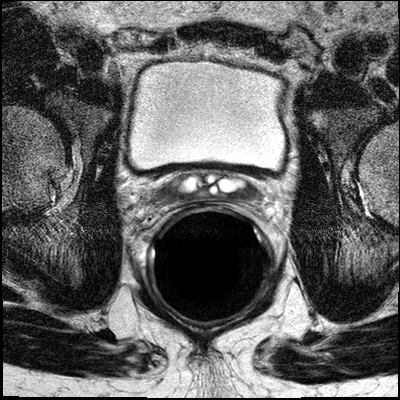
Prostate MRI examination; 3 images, each a single mid-volume slice chosen by position (not for content). Treatment context recorded for this patient: Surgery.
Image 1: axial T2-weighted image, slice 17 of 32.
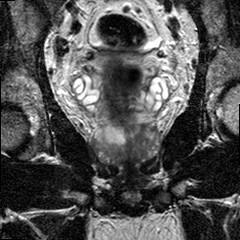
Image 2: coronal T2-weighted image, series "T2W_TSE_COR", slice 13 of 24.
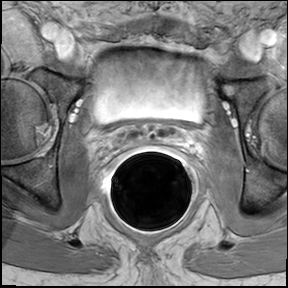
Image 3: DCE (dynamic gadolinium-enhanced) axial slice, series "AX BLISS_GAD_8", slice 17 of 32, dynamic phase 5 of 8, 6 mm slice thickness.
Report of this MRI examination:
FINDINGS: The prostate gland measures 4.8 (TV) x 3.1 (AP) x 3.3 (CC) cm and the prostate volume measures 25.5 cc.The zonal anatomy of the prostate gland is preserved. In the base and mid-third of the left posterolateral peripheral zone, geographic areas of low T2 hypointensity are visualized from the 4-6 o'clock positions with associated suspicious wash-in and washout genetics on dynamic postgadolinium images. The dominant nodule measures 1.8 (TV) x 0.8 (AP) cm in maximal dimension. The left posterolateral mass closely approximates the left neurovascular bundle with no definite involvement. No definite extracapsular involvement is seen. Rectum wall and Bladder neck are unremarkable. Mild benign prostatic hypertrophy and chronic prostatitis are visualized. The seminal vesicles are unremarkable. A small 4 mm round left perirectal lymph node is visualized to adjacent to the left obturator internus (slice location 48, series 601). No obturator or iliac lymphadenopathy. No suspicious bone marrow signal abnormalities are seen. Multiplanar reconstructions, subtraction images, and CAD analysis of the dynamic series for assessment of the kinetic information facilitated the interpretation of the exam. IMPRESSION:
1. Left posterolateral prostate cancer involving the base and middle third of the gland without evidence of extraglandular disease. No MRI evidence of neurovascular bundle involvement or seminal vesicle involvement. No pelvic lymphadenopathy. 2. Mild benign prostatic hypertrophy and moderate chronic prostatitis.

Prostate biopsy pathology (as recorded):
The specimen consists of multiple core fragments of brown/tan tissue measuring 0.2cm to 1.5cm in length and 0.1cm in diameter. The specimen is submitted entirely in seven cassettes.1-right pz, 2-right pz/tz, 3-right apex, 4-left pz, 5-left pz/tz, 6-left apex, 7-floater. 1. RIGHT PZ: BENIGN PROSTATIC TISSUE, NO TUMOR IDENTIFIED. 2. RIGHT PZ/TZ: BENIGN PROSTATIC TISSUE, NO TUMOR IDENTIFIED. 3. RIGHT APEX: BENIGN PROSTATIC TISSUE, NO TUMOR IDENTIFIED. 4. LEFT PZ: PROSTATIC ADENOCARCINOMA, GLEASON SCORE 4+4=8/10, INVOLVING 5% OF THE TISSUE EXAMINED. 5. LEFT PZ/TZ: PROSTATIC ADENOCARCINOMA, GLEASON SCORE 4+4=8/10, INVOLVING 5% OF THE TISSUE EXAMINED. 6. LEFT APEX: BENIGN PROSTATIC TISSUE, NO TUMOR IDENTIFIED.
7. FLOATER: BENIGN PROSTATIC TISSUE, NO TUMOR IDENTIFIED

Prostatectomy specimen pathology (as recorded; the surgery followed this MRI):
Specimen(s) Received A: RIGHT PELVIC LYMPH NODES B: LEFT PELVIC LYMPH NODES C: PROSTATE GLAND Gross Description The specimens are received in three containers labeled with the patient' s name, hospital number and A. "Right Pelvic Lymph Nodes", B. "Left Pelvic Lymph Nodes" and C. "Prostate Gland". Specimen A consists of a 2.5x2.5x2 cm aggregate of fibrofatty tissue from which single whole possible lymph node dissected. The entire specimen is submitted in cassettes as follows: A1 multiple lymph nodes, A2 remaining fibroadipose tissue. Specimen B consists of a 3x2x0.5 cm aggregate of fibrofatty tissue from which four whole lymph nodes dissected. The entire specimen is submitted in cassettes as follows: B1 three whole lymph nodes, B2 single whole lymph node, B3 remaining fibroadipose tissue. Specimen C consists of a 38.5 grams, 4x2.5x2 cm radical prostatectomy specimen. The attached right and left vas measuring 4.5 cm in length by 0.4 cm in diameter, right and left seminal vesicles average 4x3x0.5 cm. The specimen is inked as follows: right side black, left side blue. Proximal and distal margins are taken and radial sectioned. The specimen is transversely sectioned to reveal a vaguely nodular surface. The entire prostate is submitted in cassettes as follows: C1 and C2 radial section, proximal base of bladder margin, C3 and C4 radial section, distal ureteral margin, C5 thru C8 entire right anterior lobe, distal to proximal, C9 thru C12 entire right posterior lobe, distal to proximal, C13 thru C15 entire left posterior lobe, distal to proximal, C16 thru C18 entire left anterior lobe, distal to proximal, C19 right seminal vesicle and right vas, C20 left seminal vesicle and left vas.
Final Diagnosis A.RIGHT PELVIC LYMPH NODES: SEVEN (7) REACTIVE LYMPH NODES, NO TUMOR IDENTIFIED. B.LEFT PELVIC LYMPH NODES: TEN (10) REACTIVE LYMPH NODES, NO TUMOR IDENTIFIED. C.PROSTATE GLAND: Procedure: Radical Prostatectomy Prostate Size: 4x2.5x2cm. Weight: 38.5 grams Lymph Node Sampling: Pelvic lymph node dissection Histologic Type: Adenocarcinoma (acinar type) Histologic Grade: Gleason Score Primary Pattern: 4 Secondary Pattern: 4 Total Gleason Score: 4+4=8/10 Tumor Quantitation / Proportion of prostate involved by tumor: Approximately 6%
Extraprostatic Extension: Not identified Seminal Vesicle Invasion: Not identified Margins: Margins uninvolved by invasive carcinoma Treatment Effect on Carcinoma: Not identified Lymph-Vascular Invasion: Not identified Perineural Invasion: Present Additional Pathologic Findings: Chronic Inflammation AJCC Pathologic Staging: (pT2c, pNx, pMx) pT2c: Bilateral disease pN0: No regional lymph node metastasis Specify: Number examined:17 Number involved:0 pMx: Not applicable
Pin-4 and AE1/3 immunostains (on block C13) support the diagnosis of no extraprostatic extension.
Clinical diagnosis and History: Prostate Ca